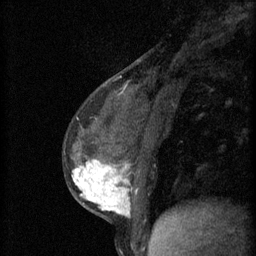
Breast MRI (dynamic contrast-enhanced), one sagittal slice. Position 24 of 60 along the scan axis. 3 images stored at this slice position (order not interpretable as contrast timing). 1.5 T. TE 4.2 ms, TR 11 ms. 2 mm slice thickness. 256 × 256 image matrix, field of view 180 × 180 mm. Female patient, age 37 years.
Outlined on this slice (semi-automatically segmented with operator editing):
- analysis volume of interest (the breast-tissue region the enhancement analysis was run in; not a lesion): box from (x=65, y=138) to (x=174, y=221) px
- tumour enhancement mask (voxels above the 70 % enhancement threshold inside the analysis volume of interest): (x=72, y=160)–(x=130, y=217)